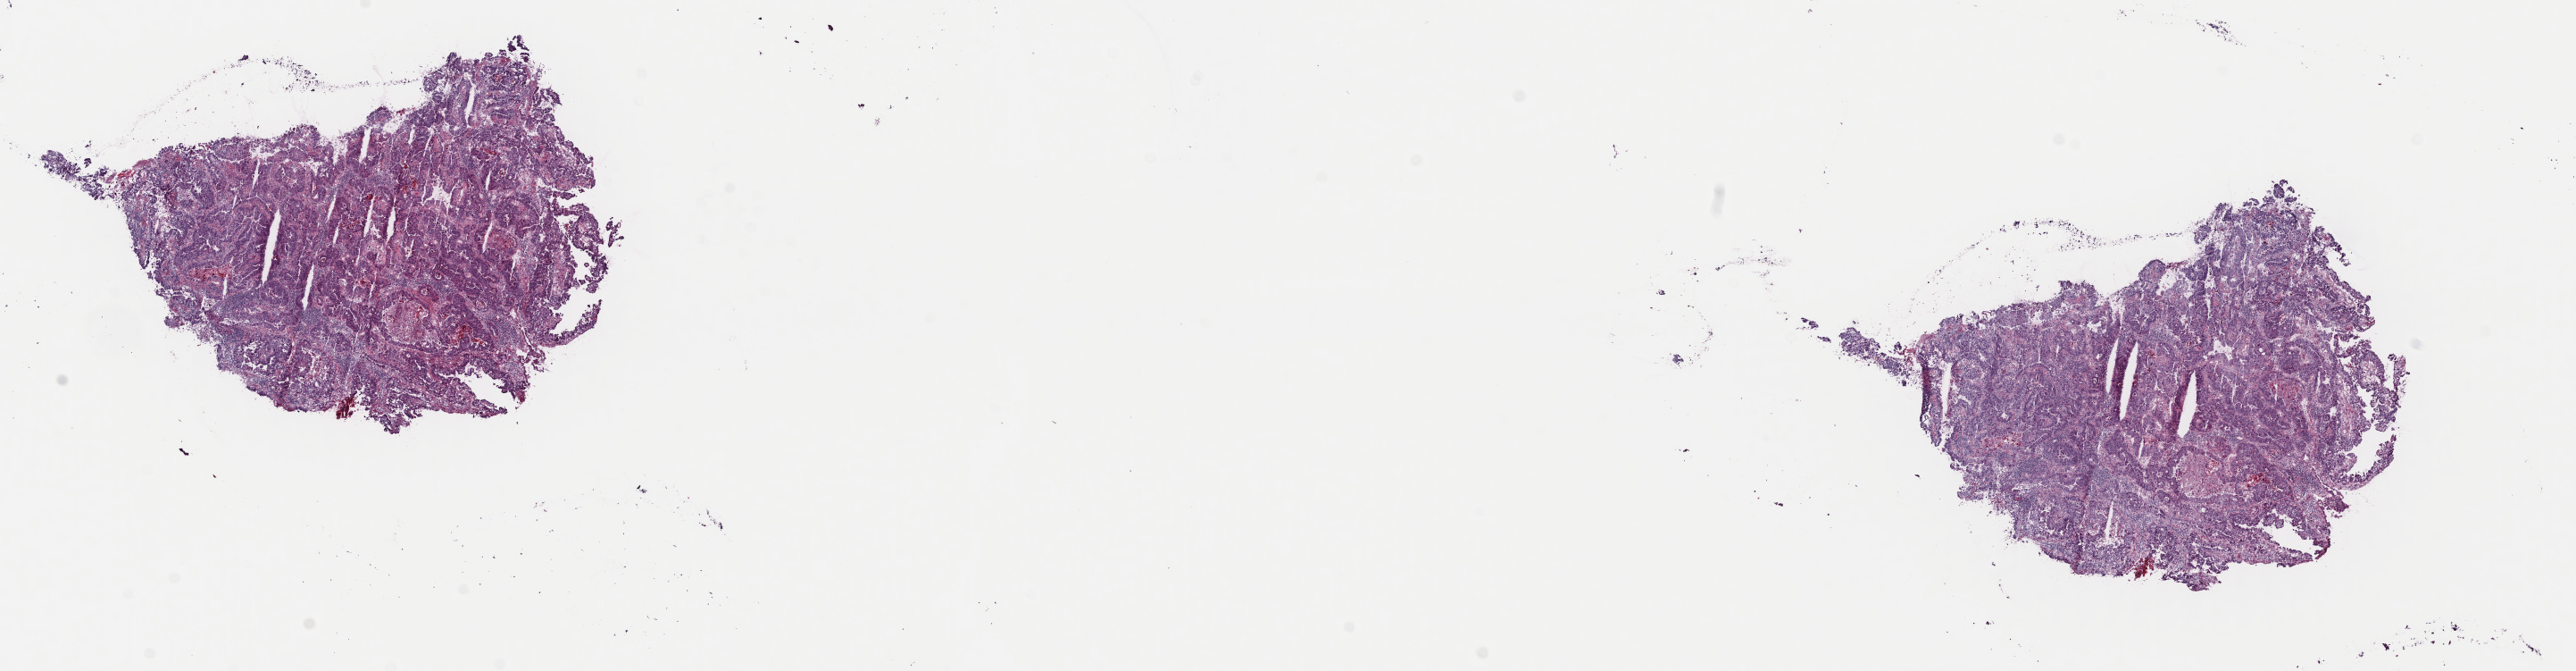
Digitized Hematoxylin and eosin (H&E) stained tissue section (whole slide) — whole scanned area (about 22.8 x 5.9 mm) shown as a low-resolution overview. Frozen section. Sample: primary tumour, colon. Female patient; age at initial diagnosis 71 years. Composition of this section per pathologist review: tumour cells 70%, tumour nuclei 70%, normal cells 0%, stromal cells 25%, necrosis 5%. Inflammatory infiltration, as recorded: lymphocyte infiltration 2%, monocyte infiltration 2%, neutrophil infiltration 5%.
Lymph nodes positive (case pathology): 7 of 13 examined. TNM: T3 N2b MX. AJCC pathologic stage: IIIC (7th edition). Pathologic diagnosis: Adenocarcinoma, NOS (transverse colon).